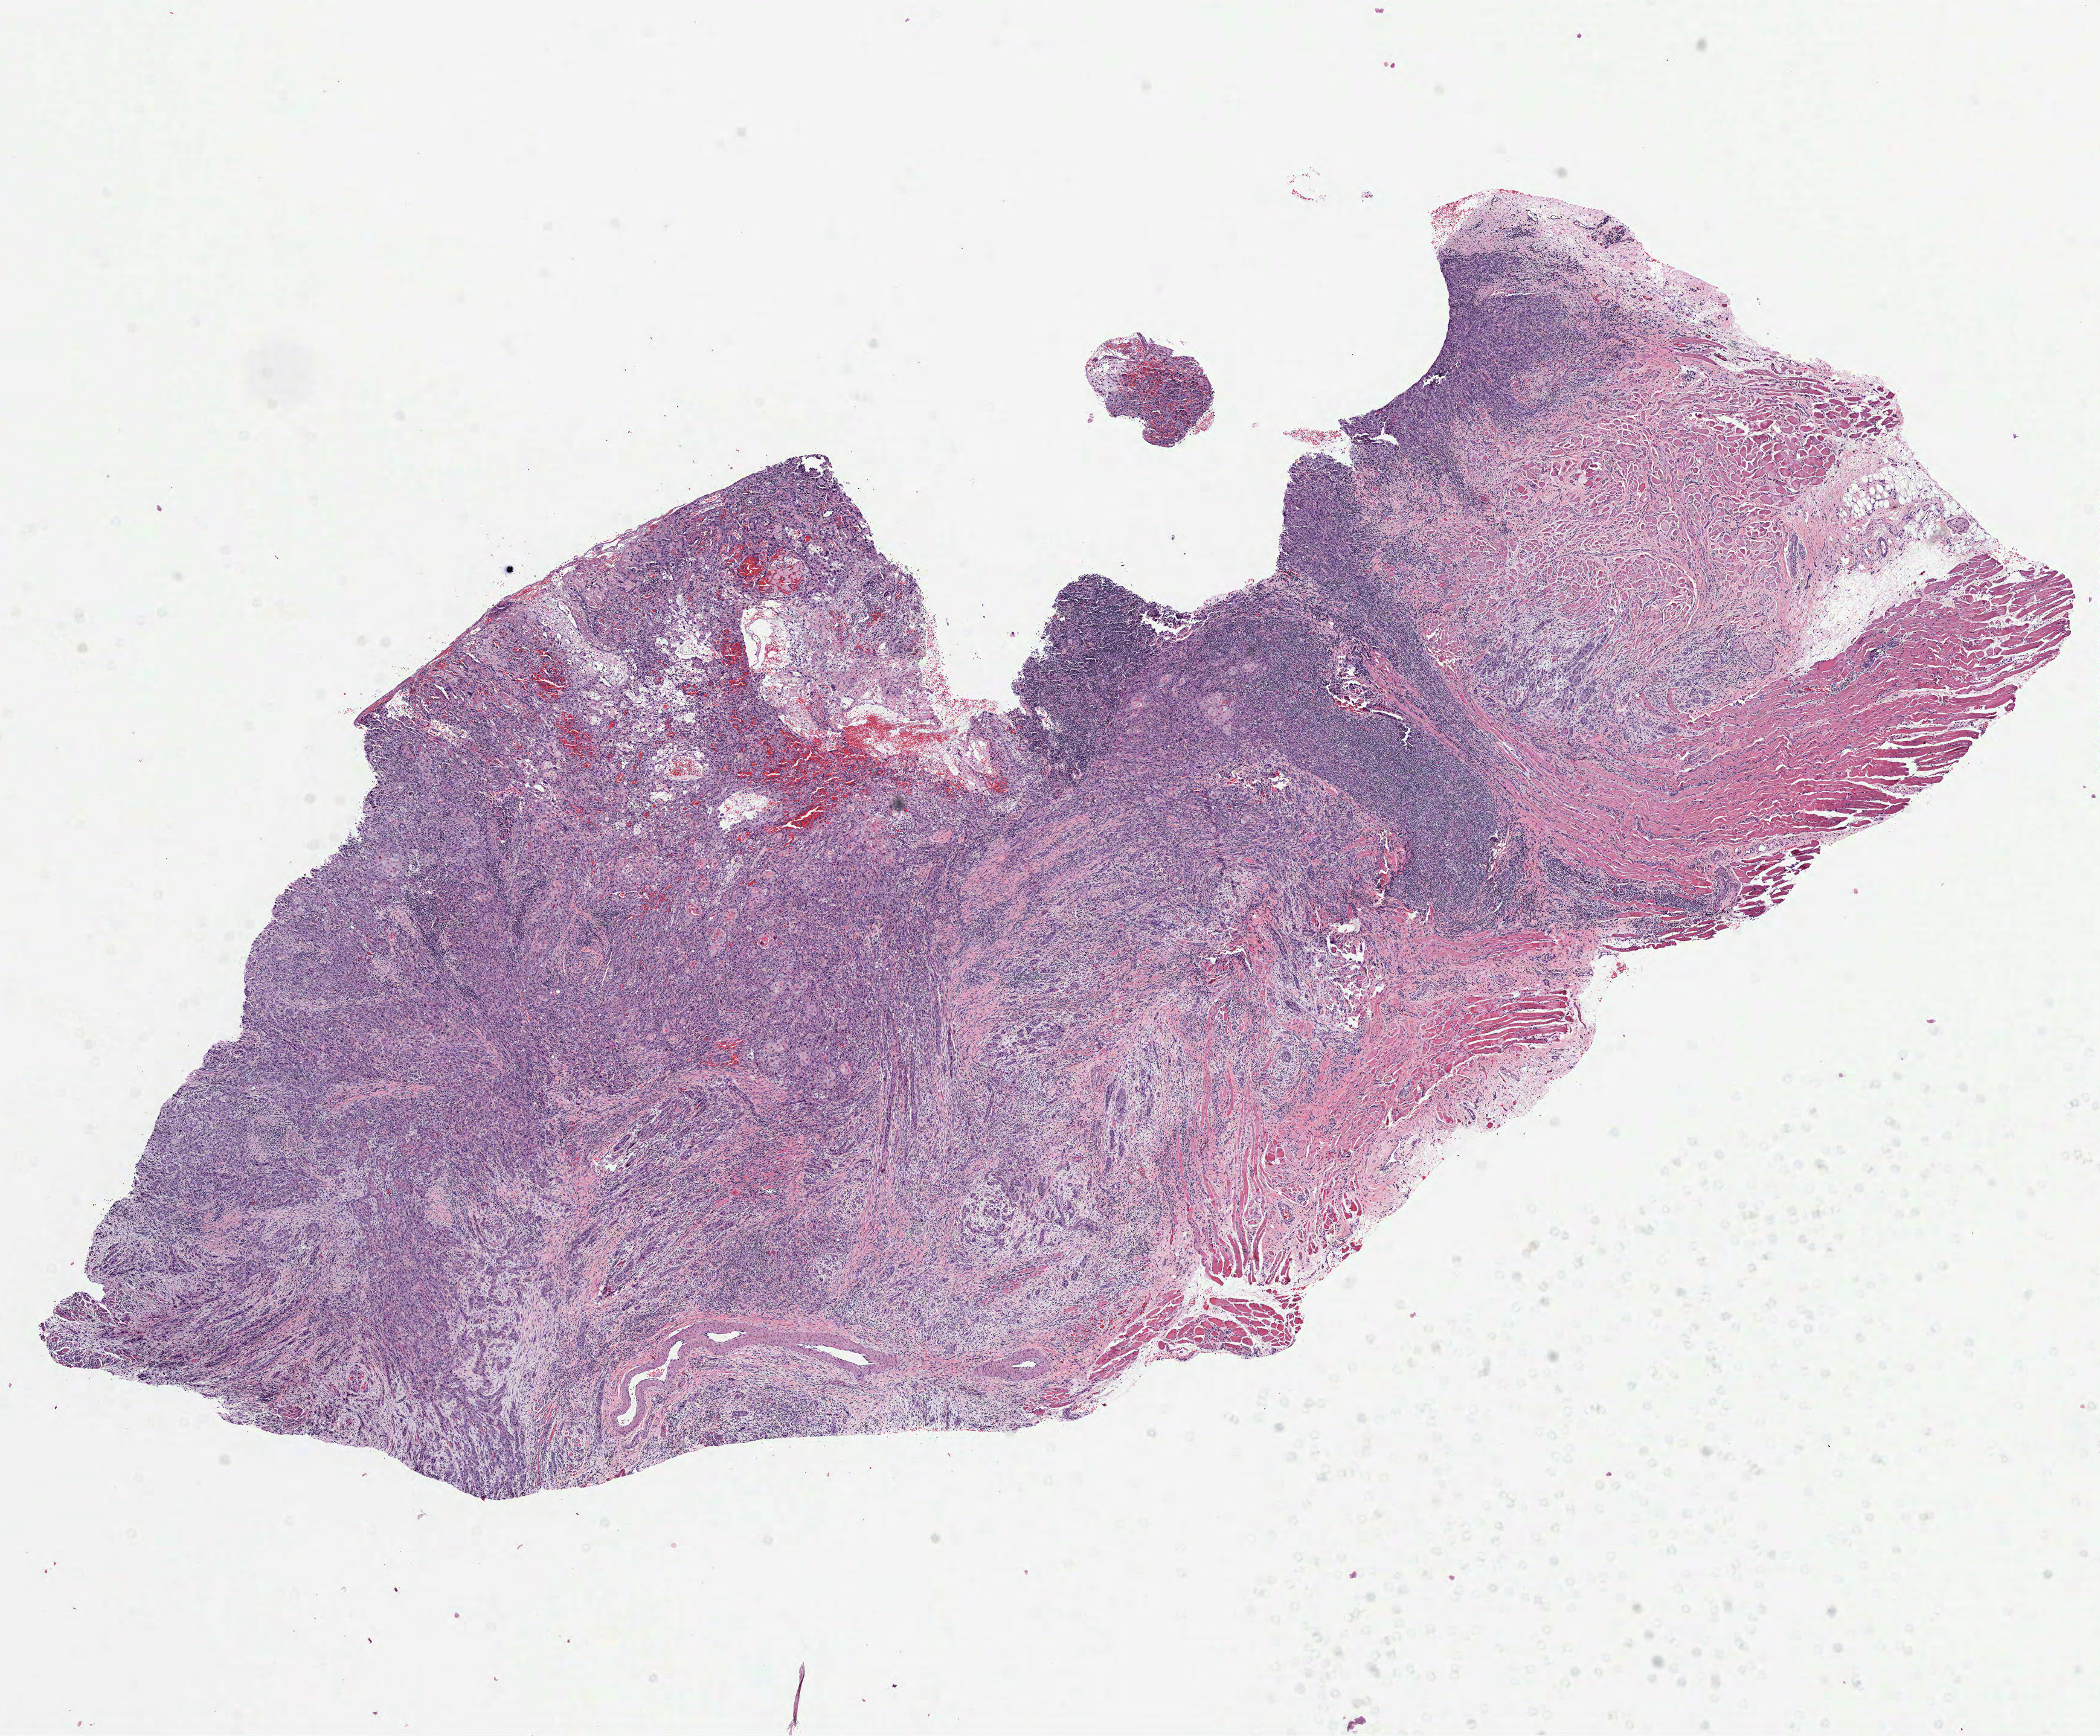
H&E-stained whole-slide image, a low-resolution overview of the entire scanned area, about 14.0 x 11.6 mm (acquisition: 40x scan). Formalin-fixed paraffin-embedded (FFPE) diagnostic section. Primary tumour sample from the head and neck. Patient: male, age at initial diagnosis 61 years. Histologic grade: G3 (poorly differentiated).
Histologic diagnosis: Squamous cell carcinoma, NOS (tongue, NOS). AJCC pathologic stage: III.